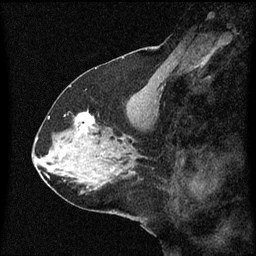
Breast MRI (dynamic contrast-enhanced), one sagittal slice; slice 28 of 60 in the series (ordered by position); dynamic contrast-enhanced series, image 2 of 3 at this slice position (ordered by acquisition); 1.5 T; TE 4.2 ms, TR 8.4 ms; 2 mm slice thickness; 256 × 256 image matrix, field of view 200 × 200 mm. Female patient, age 59 years.
Outlined on this slice (semi-automatic segmentation, software-assisted and operator-edited):
- analysis volume of interest (the breast-tissue region the enhancement analysis was run in; not a lesion): box from (x=70, y=112) to (x=99, y=137) px
- tumour enhancement mask (voxels above the 70 % enhancement threshold inside the analysis volume of interest): (x=76, y=112)–(x=95, y=129)